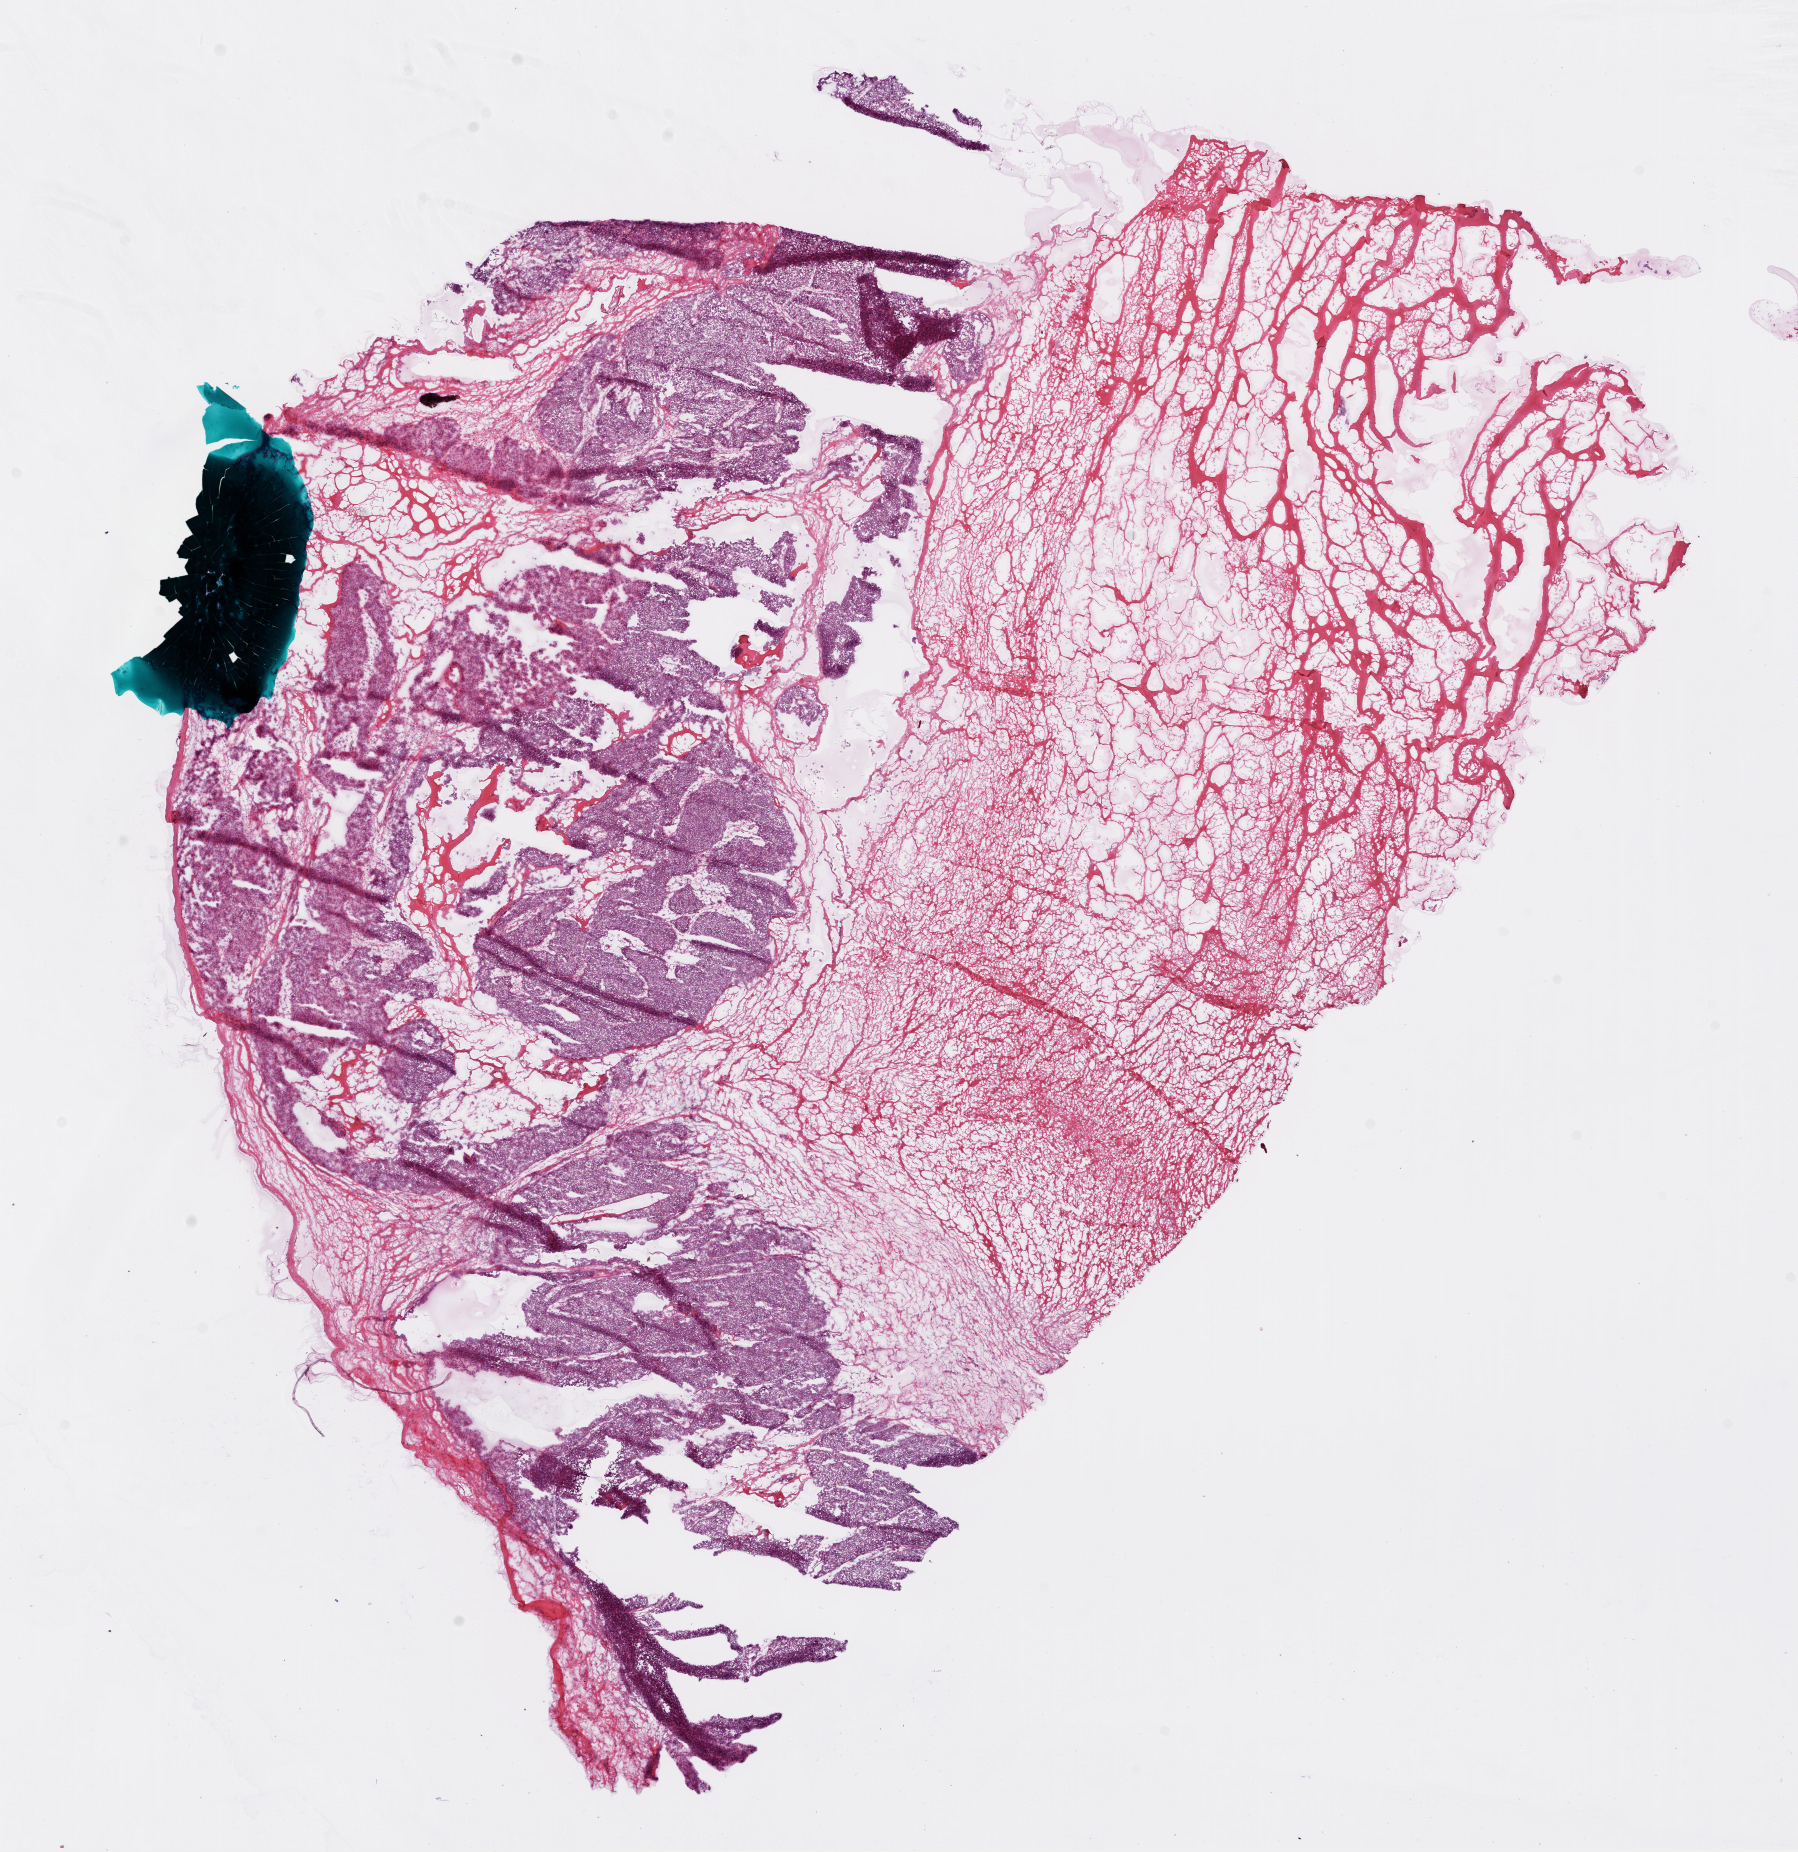
Hematoxylin and eosin (H&E) stained whole-slide image, shown as a low-resolution overview of the whole scanned area (about 14.5 x 14.9 mm), frozen section from the bottom of the tissue portion, sample: primary tumour, ovary. Patient: female, age at initial diagnosis 56 years. Histologic grade: G3 (poorly differentiated). Pathologist review of this section (percent, as recorded): tumour nuclei 90%, necrosis 1%.
- diagnosis: Serous cystadenocarcinoma, NOS
- FIGO stage: IV